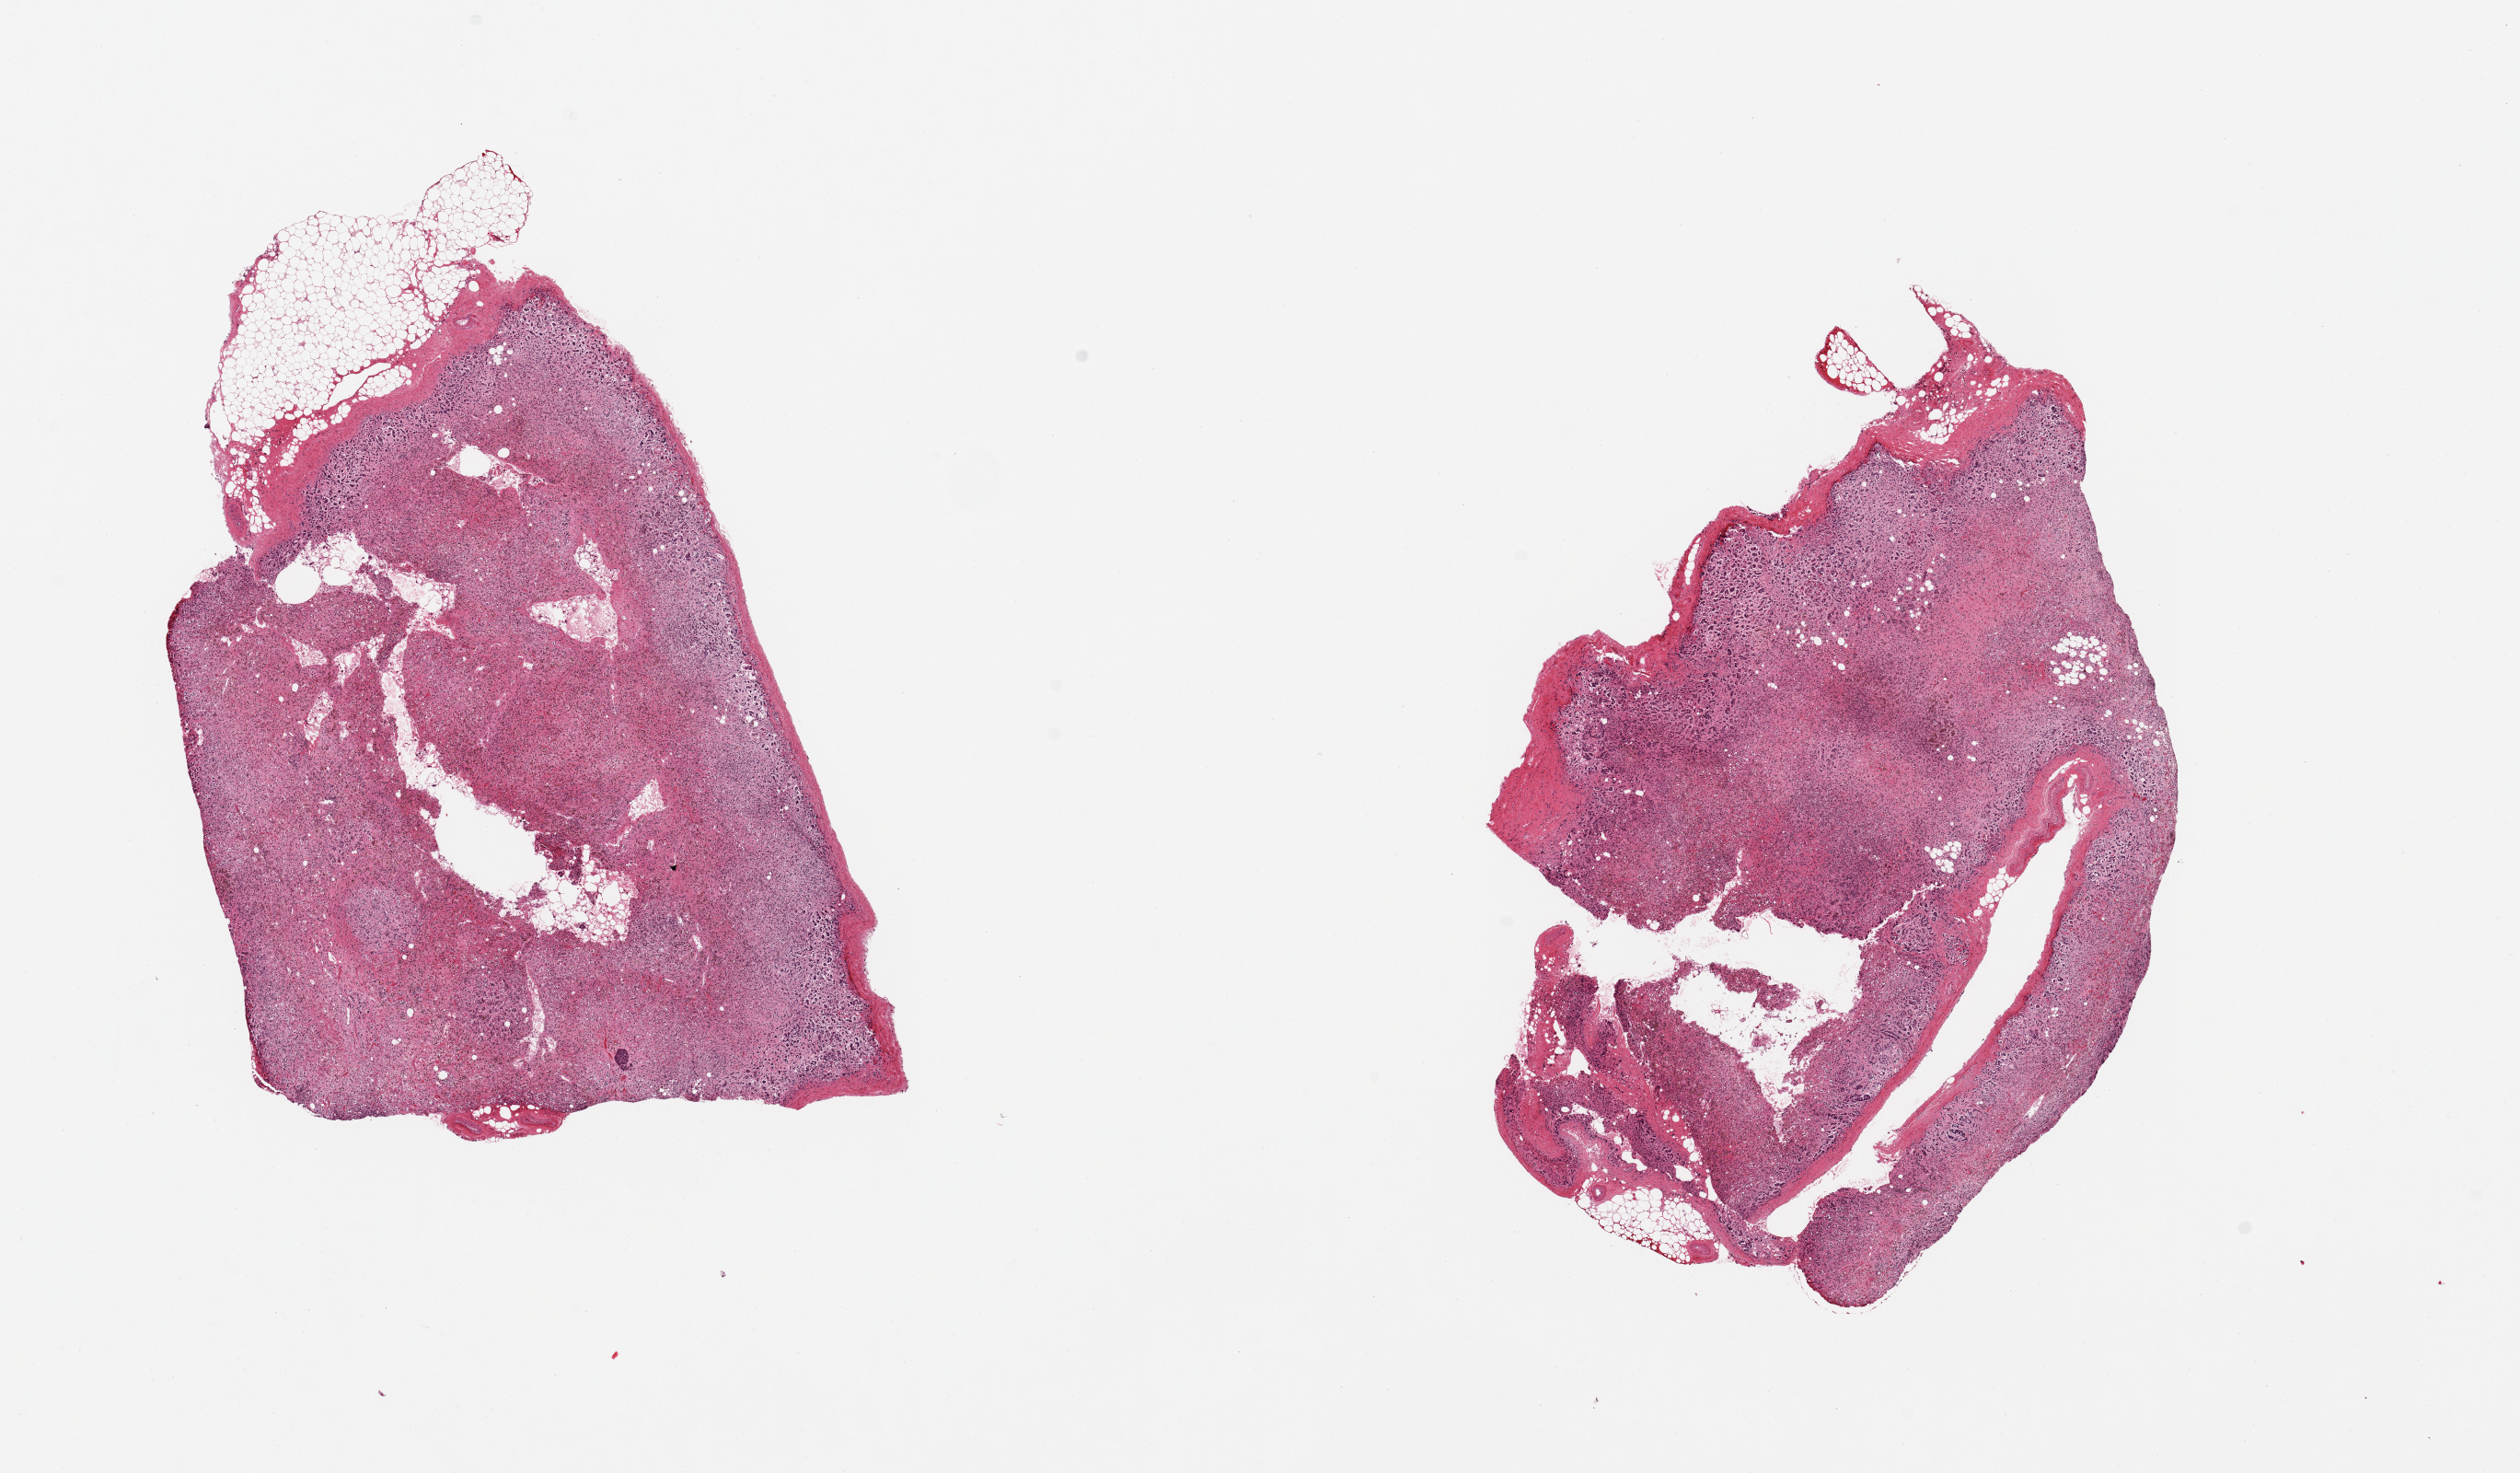
H&E whole-slide image — shown as a low-resolution overview of the whole scanned area (about 21.7 x 12.7 mm). PAXgene-fixed paraffin-embedded (PFPE) section. Section of adrenal gland (target tissue). Donor tissue sample. Male donor.
Reviewer comment on this tissue sample: 2 pieces, all cortex, badly autolyzed, adherent nubbin of fat on one, ~1mm.